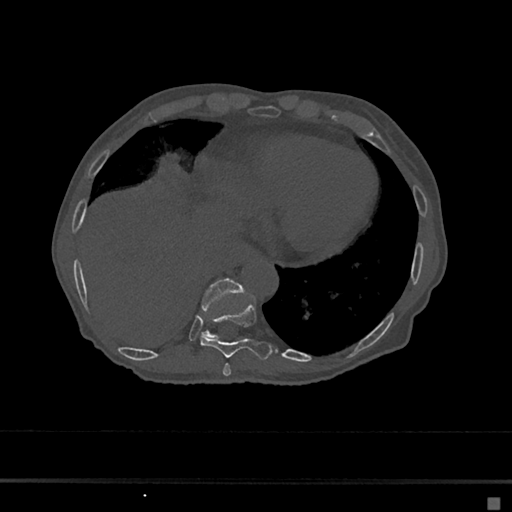
CT including the spine, one axial slice. Position 263 of 797 along the scan axis. 120 kVp. Bone window (W 1800 / L 400 HU). 0.5 mm slice thickness. 512 × 512 image matrix, field of view 360 × 360 mm. Female patient, age 68 years. From the clinical record (not read from this slice): primary cancer: renal.
Outlined on this slice (semi-automatic segmentation, software-assisted and operator-edited):
- T10 vertebra: bounding box (x1, y1, x2, y2) in pixels: (201, 278, 244, 339)
- T8 vertebra: (223, 363, 231, 376)
- T9 vertebra: (200, 302, 273, 360)